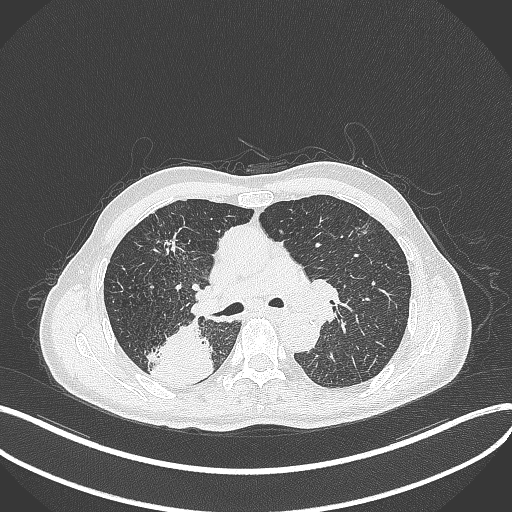
Chest CT, one axial slice. Slice 283 of 428 in the series (ordered by position). Reconstruction kernel B70f. 120 kVp. Lung window (W 1500 / L -600 HU). 512 × 512 image matrix, field of view 400 × 400 mm. Male patient, age 79 years. From the clinical record (not read from this slice): clinical TNM (as recorded): T3 N0 M0.
Outlined on this slice (rectangle marked by the reading radiologist):
- lung tumour (recorded histology: adenocarcinoma): bounding box <148,321,213,385> (left, top, right, bottom; pixels)